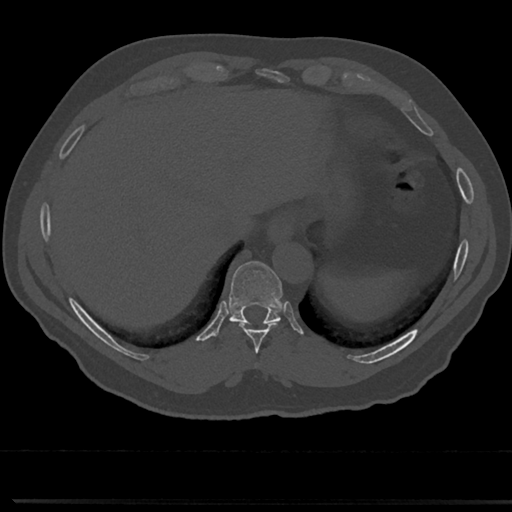
CT including the spine, one axial slice. Position 280 of 817 along the scan axis. Reconstruction kernel Br40s/3. Bone window (W 1800 / L 400 HU). 0.5 mm slice thickness. 512 × 512 image matrix, field of view 355 × 355 mm. Patient: male, 61 years. Case-level facts recorded for this patient, not image findings: primary cancer: prostate.
Structures marked on this image (semi-automatic segmentation, software-assisted and operator-edited):
- T10 vertebra: bounding box (x1, y1, x2, y2) in pixels: (233, 316, 278, 321)
- T8 vertebra: (254, 356, 264, 371)
- T9 vertebra: (213, 262, 302, 350)